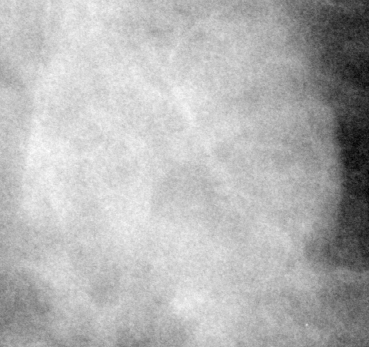
Crop from a digitized film mammogram around one marked abnormality; right breast; CC view; BI-RADS breast density category 3 (scale 1–4).
Marked abnormality: mass, shape round, margins obscured; BI-RADS assessment category 3; pathology (as recorded): benign.